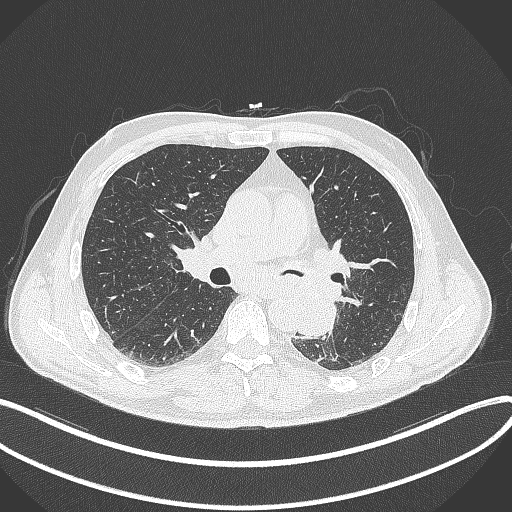
Chest CT, one axial slice; slice 196 of 329 in the series (ordered by position); reconstruction kernel B70f; lung window (W 1500 / L -600 HU); 512 × 512 image matrix, field of view 400 × 400 mm. Patient: male, 59 years. Case-level facts recorded for this patient, not image findings: clinical TNM (as recorded): T2a N2 M0.
Outlined on this slice (bounding box drawn by a radiologist):
- lung tumour (recorded histology: squamous cell carcinoma): bounding box [x1, y1, x2, y2] px = [288, 285, 337, 341]